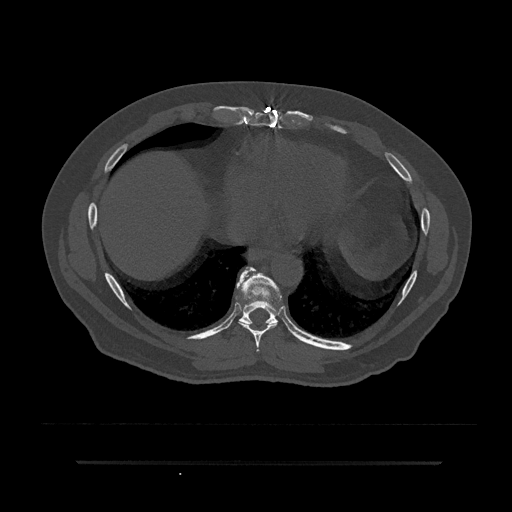
CT including the spine, one axial slice; position 403 of 797 along the scan axis; 120 kVp; bone window (W 1800 / L 400 HU); 512 × 512 image matrix, field of view 464 × 464 mm. Male patient, age 59 years. Case-level facts recorded for this patient, not image findings: primary cancer: bile ducts; vertebrae with lytic lesions (as recorded): T10.
Annotated regions visible in this slice (semi-automatically segmented with operator editing):
- T7 vertebra: bounding box (x1, y1, x2, y2) in pixels: (256, 349, 259, 352)
- T8 vertebra: (240, 267, 277, 349)
- T9 vertebra: (236, 267, 280, 331)